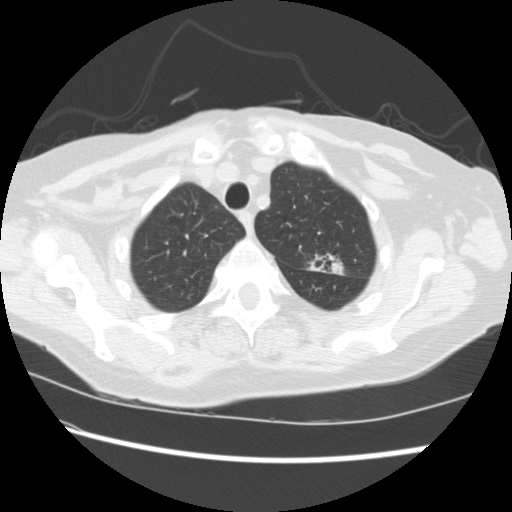
Axial slice from a low-dose chest CT screening exam; first (baseline) screen; lung window (W 1500 / L -600 HU); 2.5 mm slice thickness; 512 × 512 image matrix, field of view 340 × 340 mm. Female, age 74 years at enrolment. Former smoker at enrolment.
Lesion marked by an expert reader, bounding box (x1, y1, x2, y2) in pixels: (297, 245, 347, 284). The screening reader recorded 2 non-calcified nodules or masses ≥4 mm on this exam (left upper lobe, right lower lobe); which of them this box marks is not recorded. Official screen result: positive, change unspecified: nodule(s) >= 4 mm or enlarging nodule(s), mass(es), or other non-specific abnormalities suspicious for lung cancer. Lung cancer was diagnosed 309 days after this screen: non-small cell carcinoma, left upper lobe, stage IV (AJCC 6th edition).